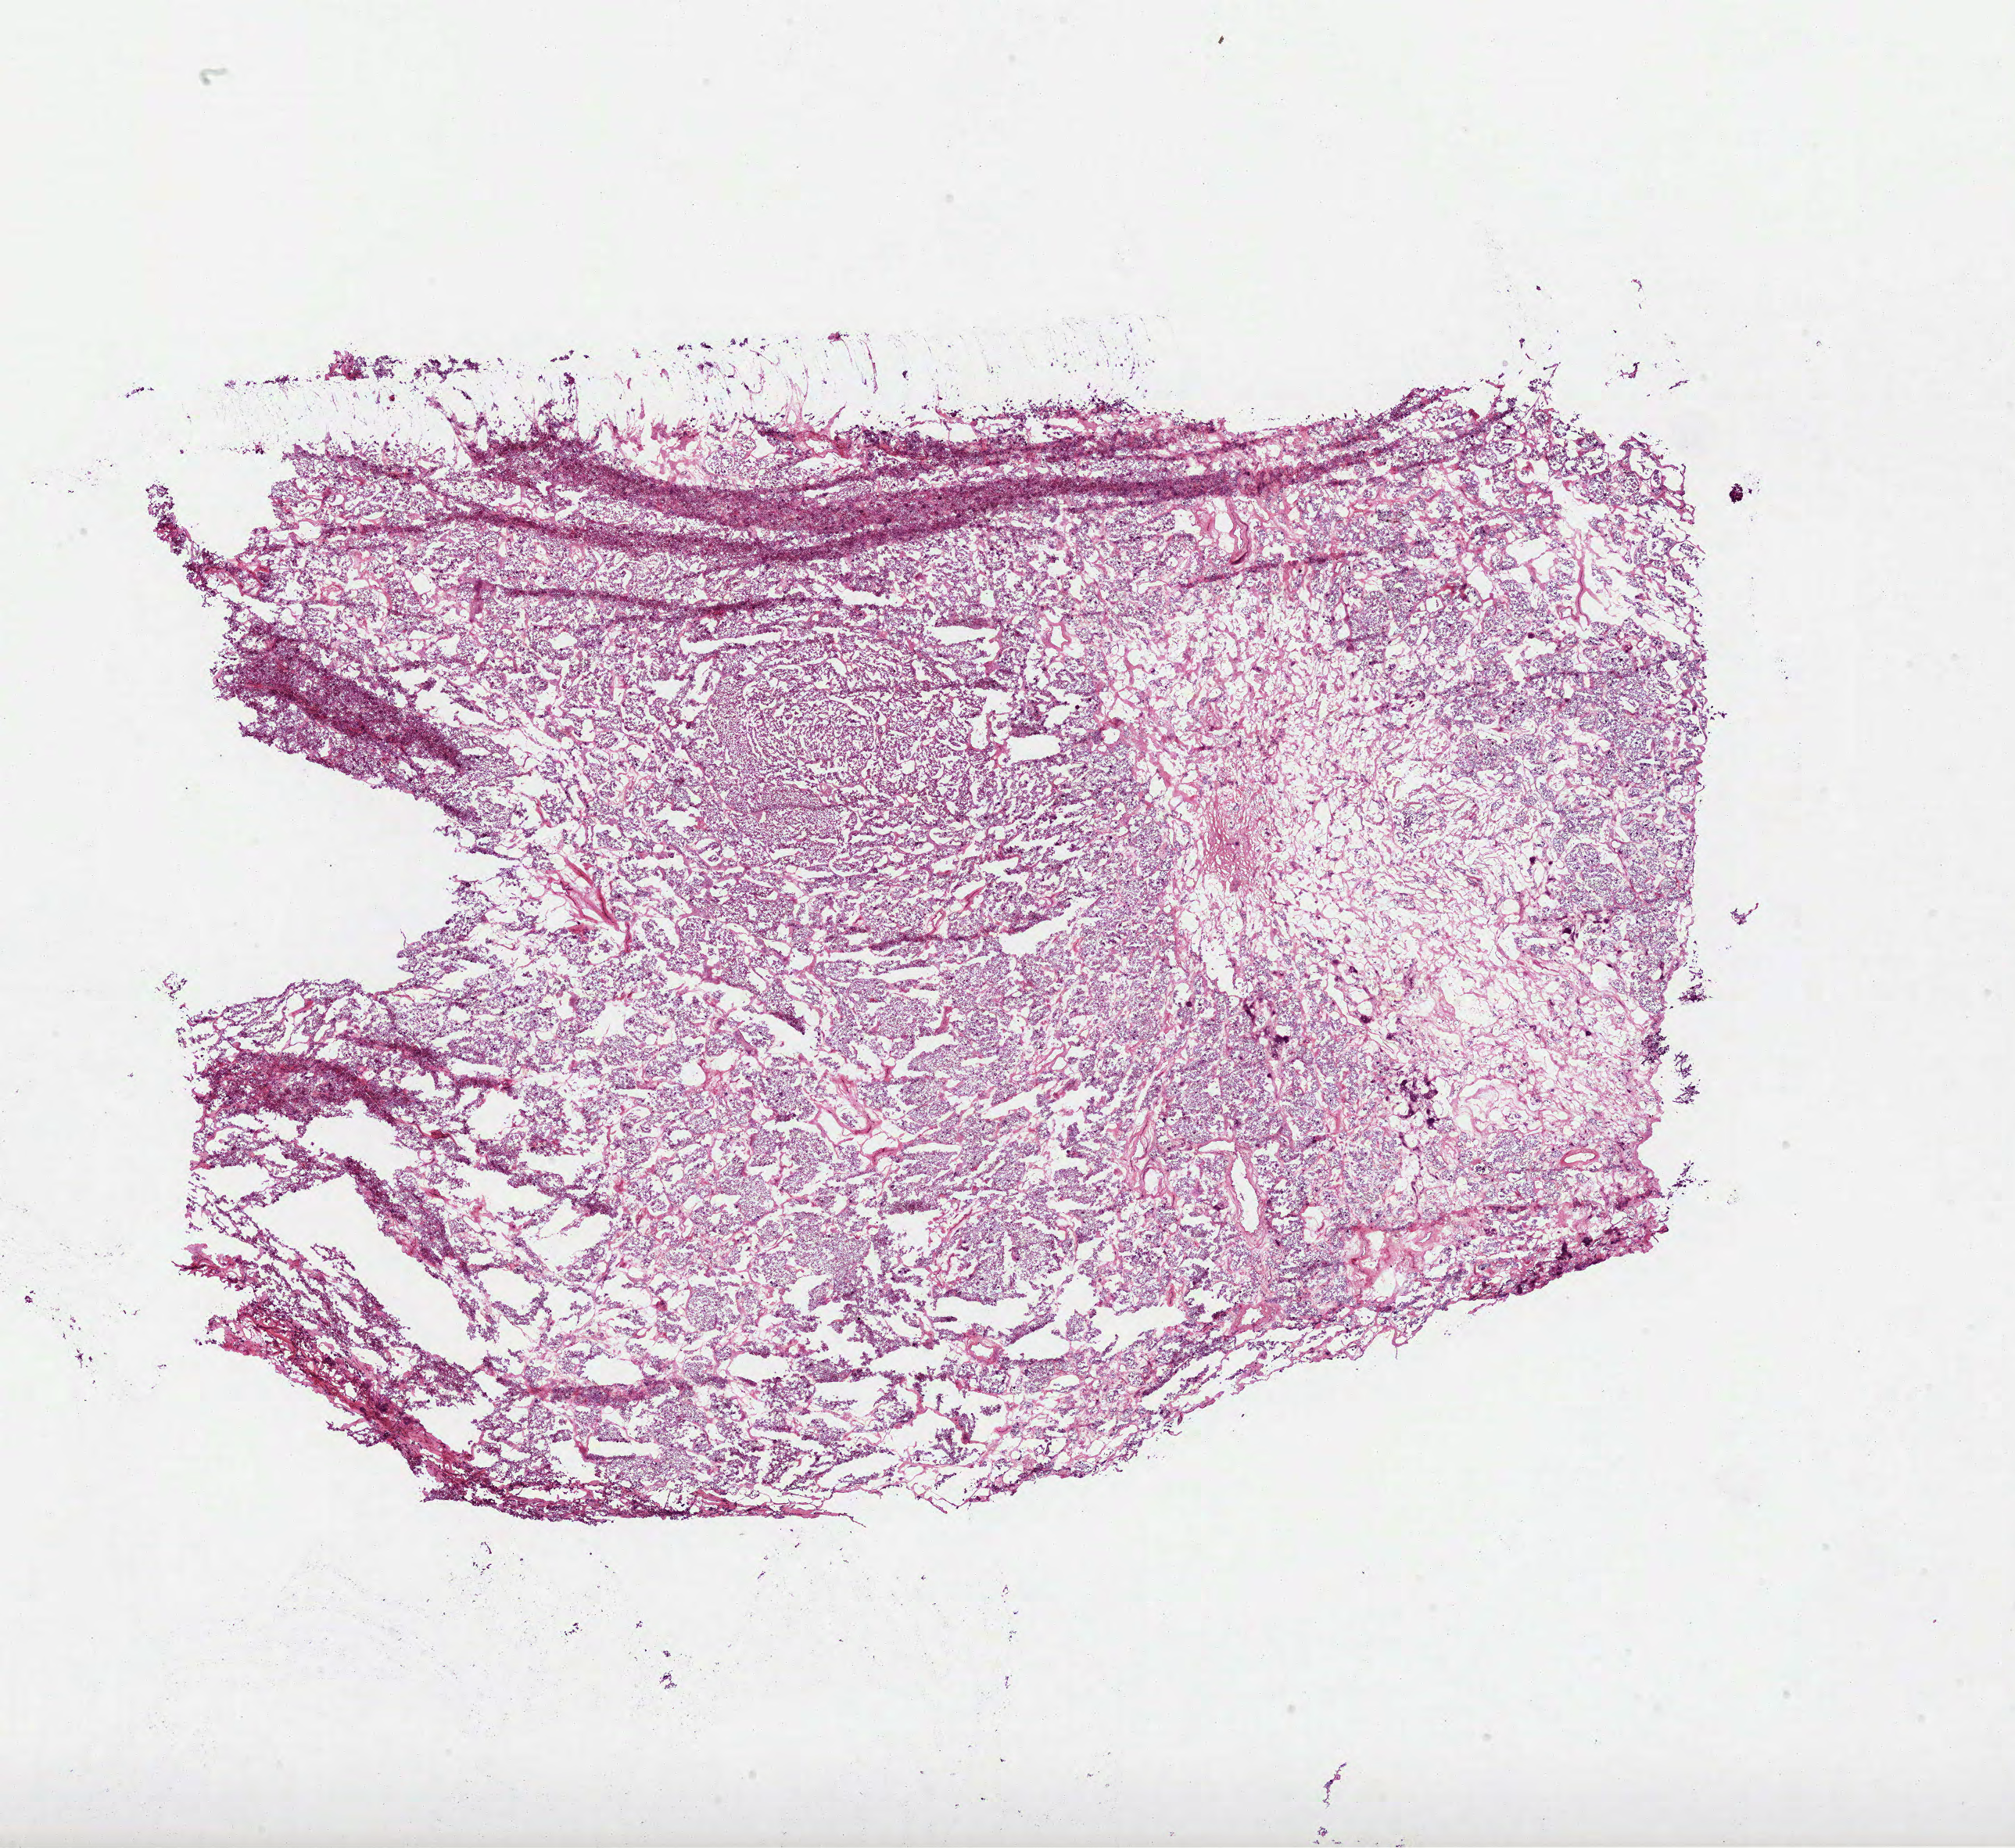
Whole-slide histology image, Hematoxylin and eosin (H&E) stained — low-resolution overview of the scanned area, about 20.8 x 19.1 mm (from a 40x scan). Frozen section from the bottom of the tissue portion. Sample: primary tumour, kidney. Patient: female, age at initial diagnosis 38 years. Composition of this section per pathologist review: tumour cells 100%, tumour nuclei 90%, normal cells 0%, stromal cells 0%, necrosis 0%. Infiltration values recorded for this section: lymphocyte infiltration 0%, monocyte infiltration 0%, neutrophil infiltration 0%.
Diagnosis: Renal cell carcinoma, chromophobe type. AJCC pathologic stage: III.